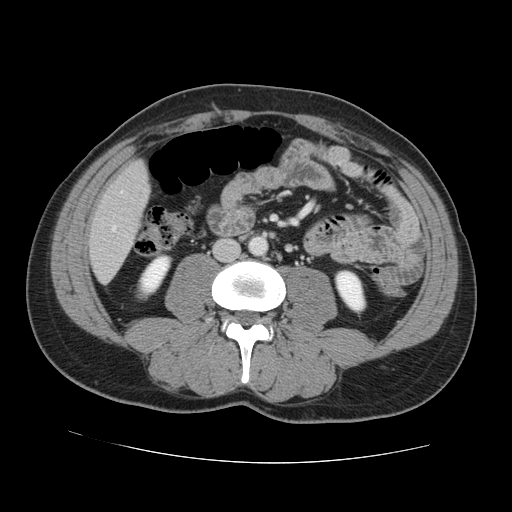
Contrast-enhanced abdominal CT, one axial slice; position 25 of 131 along the scan axis; 120 kVp; intravenous contrast given; soft-tissue window (W 400 / L 40 HU); 512 × 512 image matrix, field of view 380 × 380 mm. Male patient, age 40 years. From the clinical record (not read from this slice): diagnosis: colorectal cancer liver metastases, imaged before liver resection; multiple liver metastases: yes; largest metastasis: 2.9 cm; disease in both lobes: yes.
Annotated regions visible in this slice (outlined manually by an expert reader):
- hepatic veins: box from (x=112, y=191) to (x=122, y=231) px
- liver: (x=91, y=163)–(x=149, y=282)